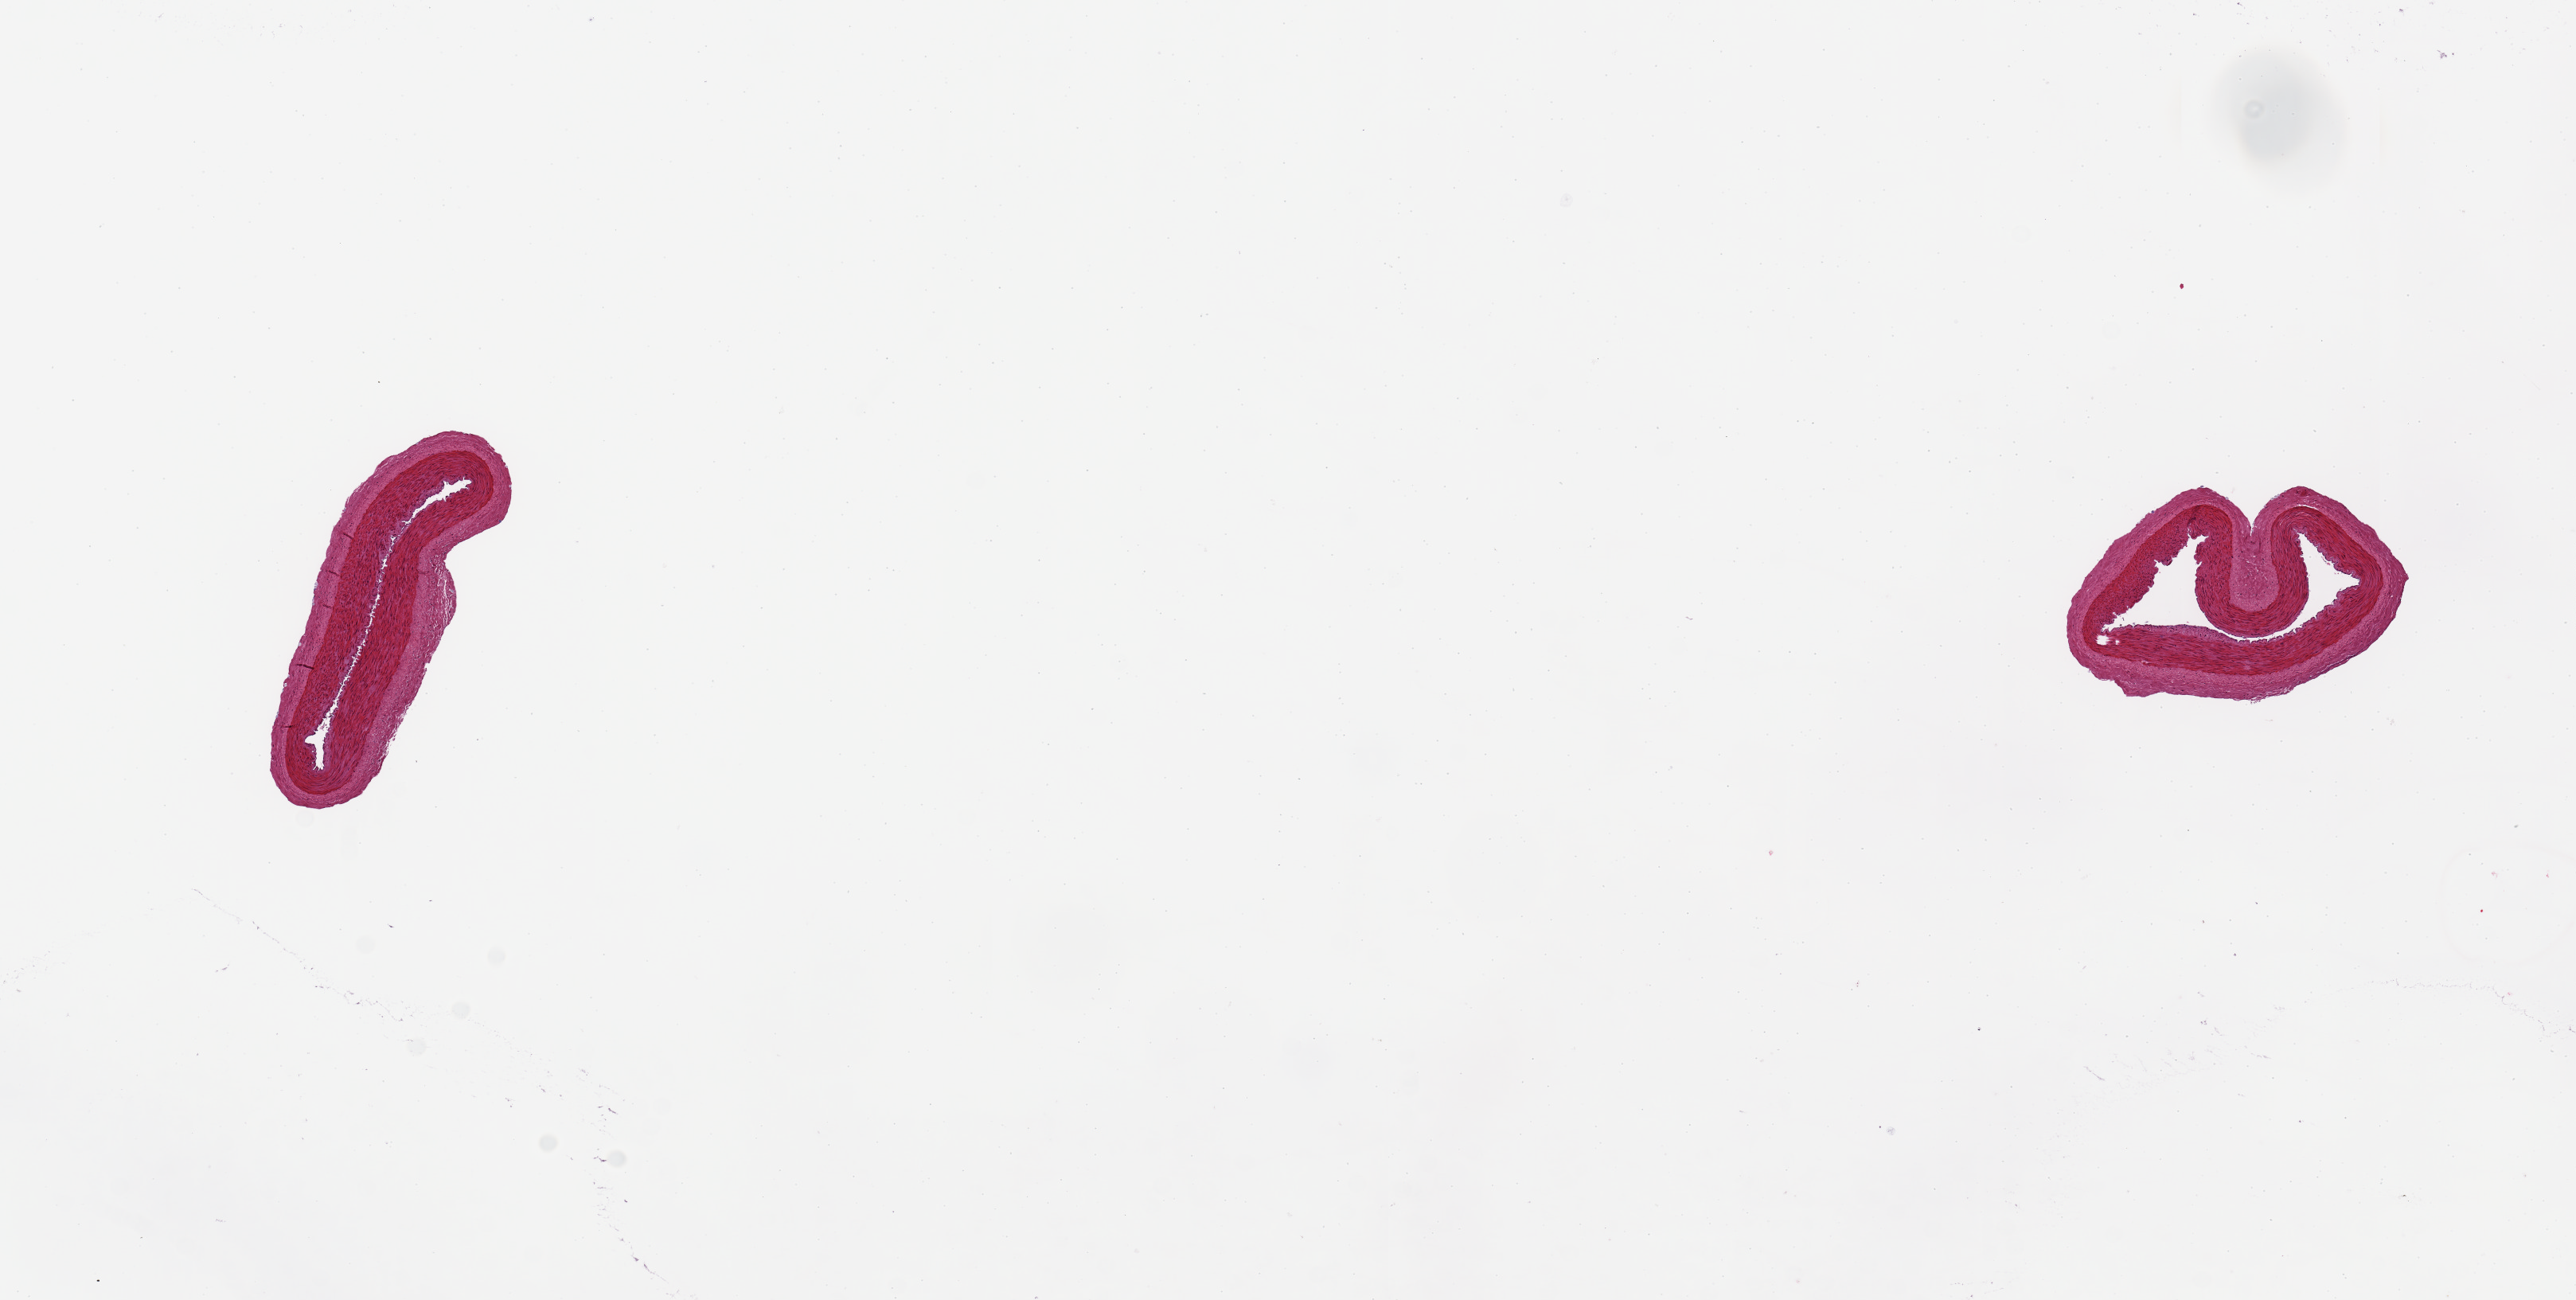
Whole-slide image, hematoxylin and eosin (H&E) stain — low-resolution overview of the scanned area, about 12.8 x 6.5 mm (acquisition: 20x scan); PAXgene-fixed, paraffin-embedded tissue; sampled site (target tissue): tibial artery; tissue donor sample.
- pathologist's review note for this sample: 2 pieces, ~2 x 0.6mm, normal artery